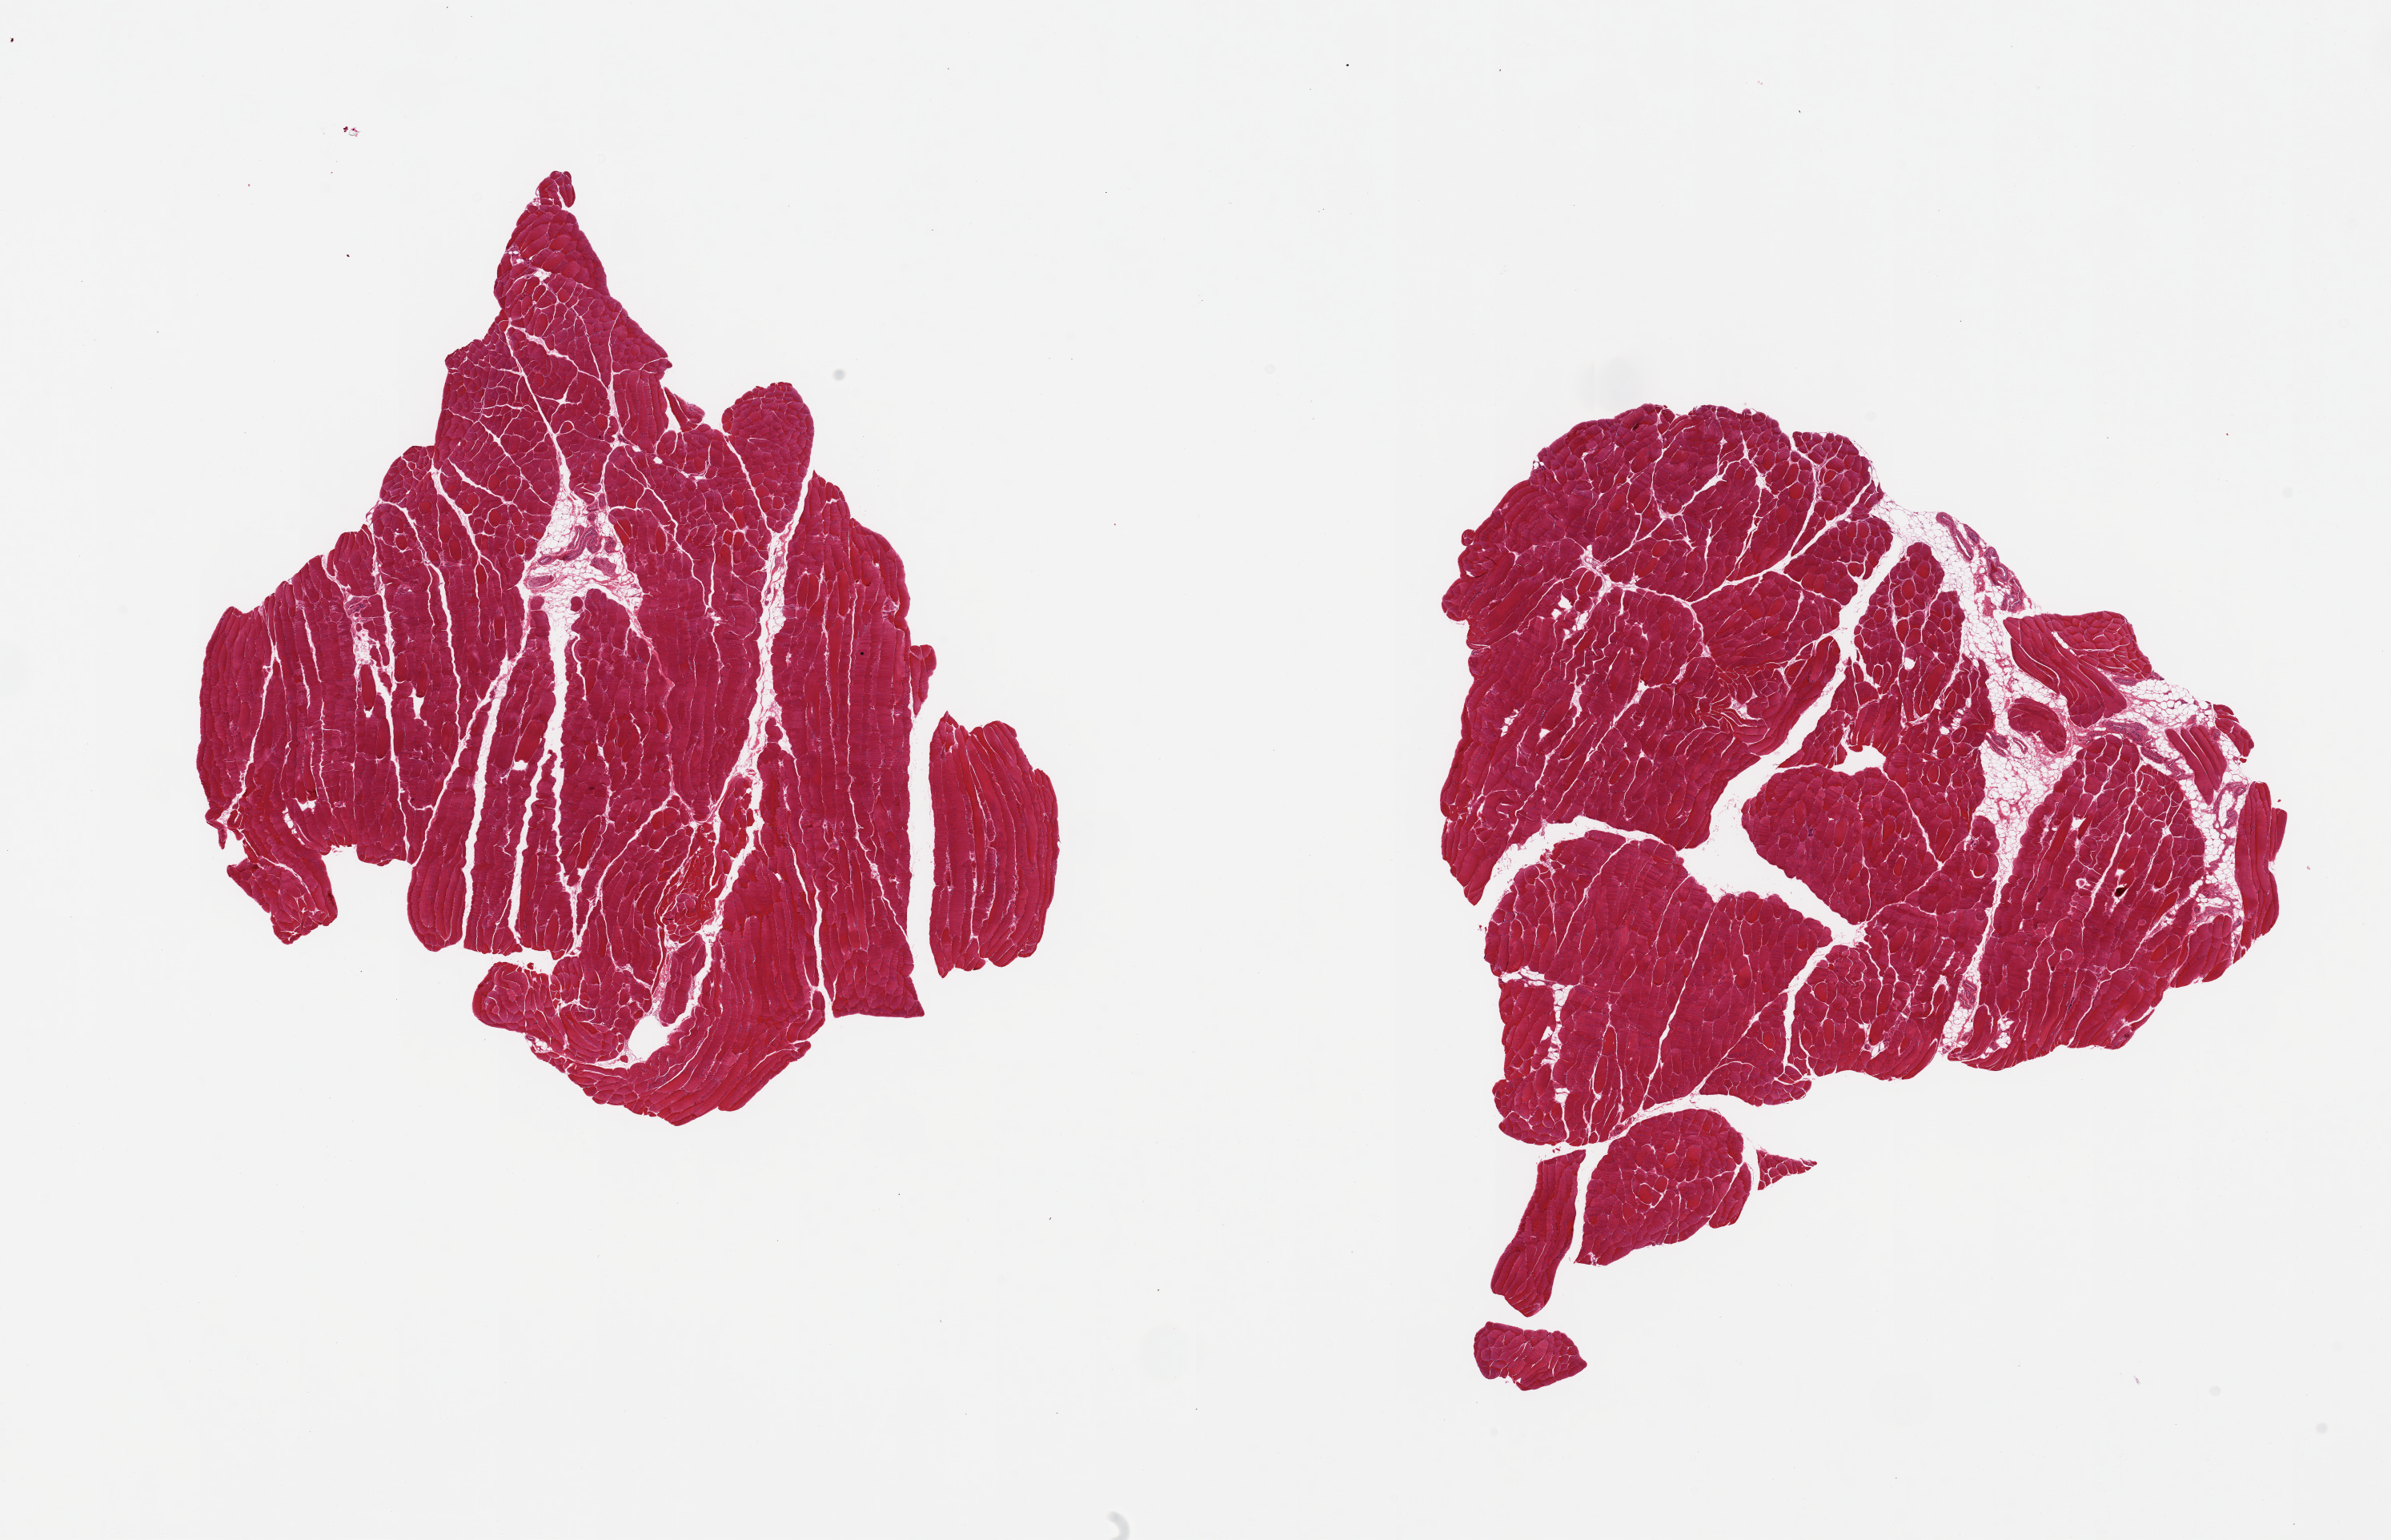
H&E whole-slide image — shown as a low-resolution overview of the whole scanned area (about 23.6 x 15.2 mm, slide scanned at 20x), PAXgene-fixed paraffin-embedded (PFPE) section, target tissue: skeletal muscle, donor tissue sample. Female donor.
- pathologist's review note for this sample: 2 pieces, ~5-10% interstitial fat